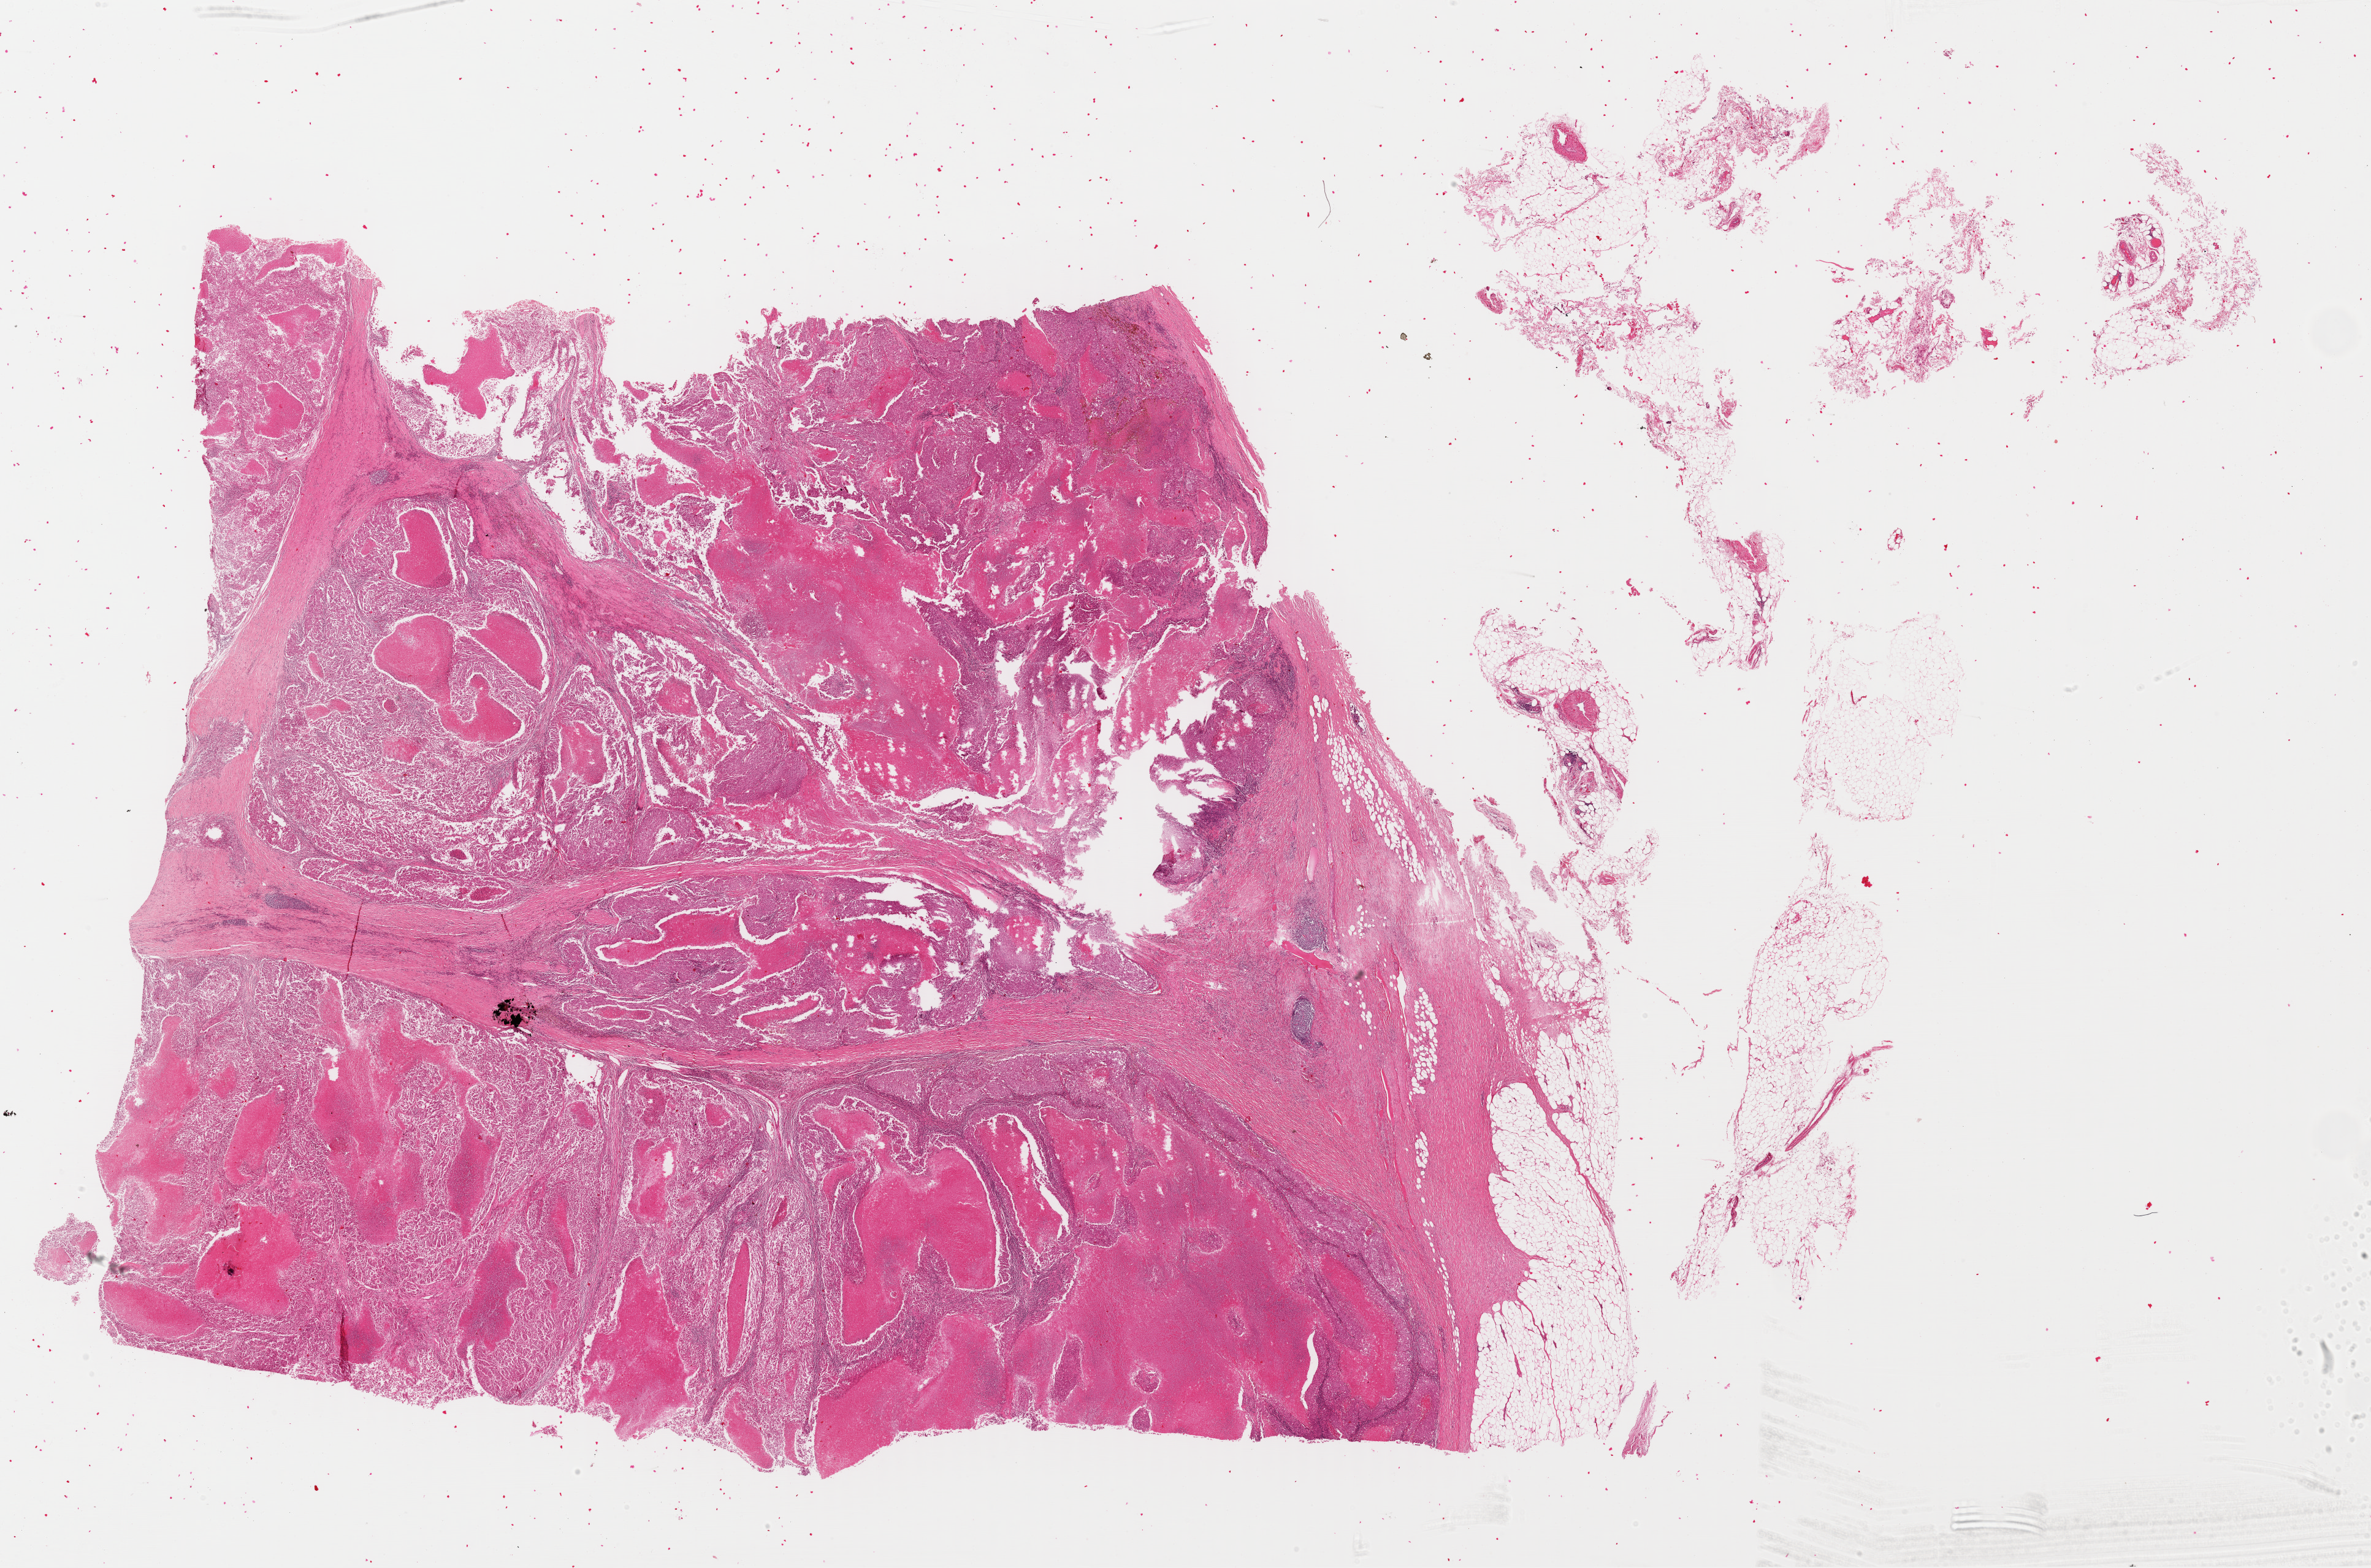
H&E whole-slide image, a low-resolution overview of the entire scanned area, about 30.5 x 20.2 mm (slide scanned at 40x), formalin-fixed paraffin-embedded (FFPE) diagnostic section, sample: primary tumour, skin. Male, age 53 years at initial diagnosis.
• histologic diagnosis: Malignant melanoma, NOS